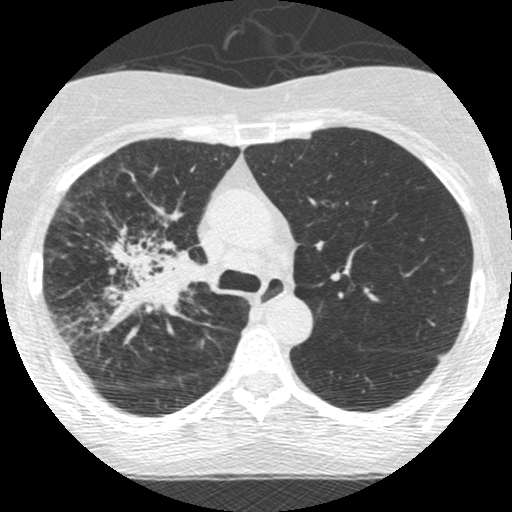
Low-dose screening chest CT, one axial slice. Position 176 of 253 along the scan axis. 120 kVp. Lung window (W 1500 / L -600 HU). 1.25 mm slice thickness. 512 × 512 image matrix, field of view 294 × 294 mm.
Annotated regions visible in this slice (manually delineated by an expert):
- lesion 2 (tumor, hilum of right lung): box from (x=103, y=222) to (x=210, y=331) px